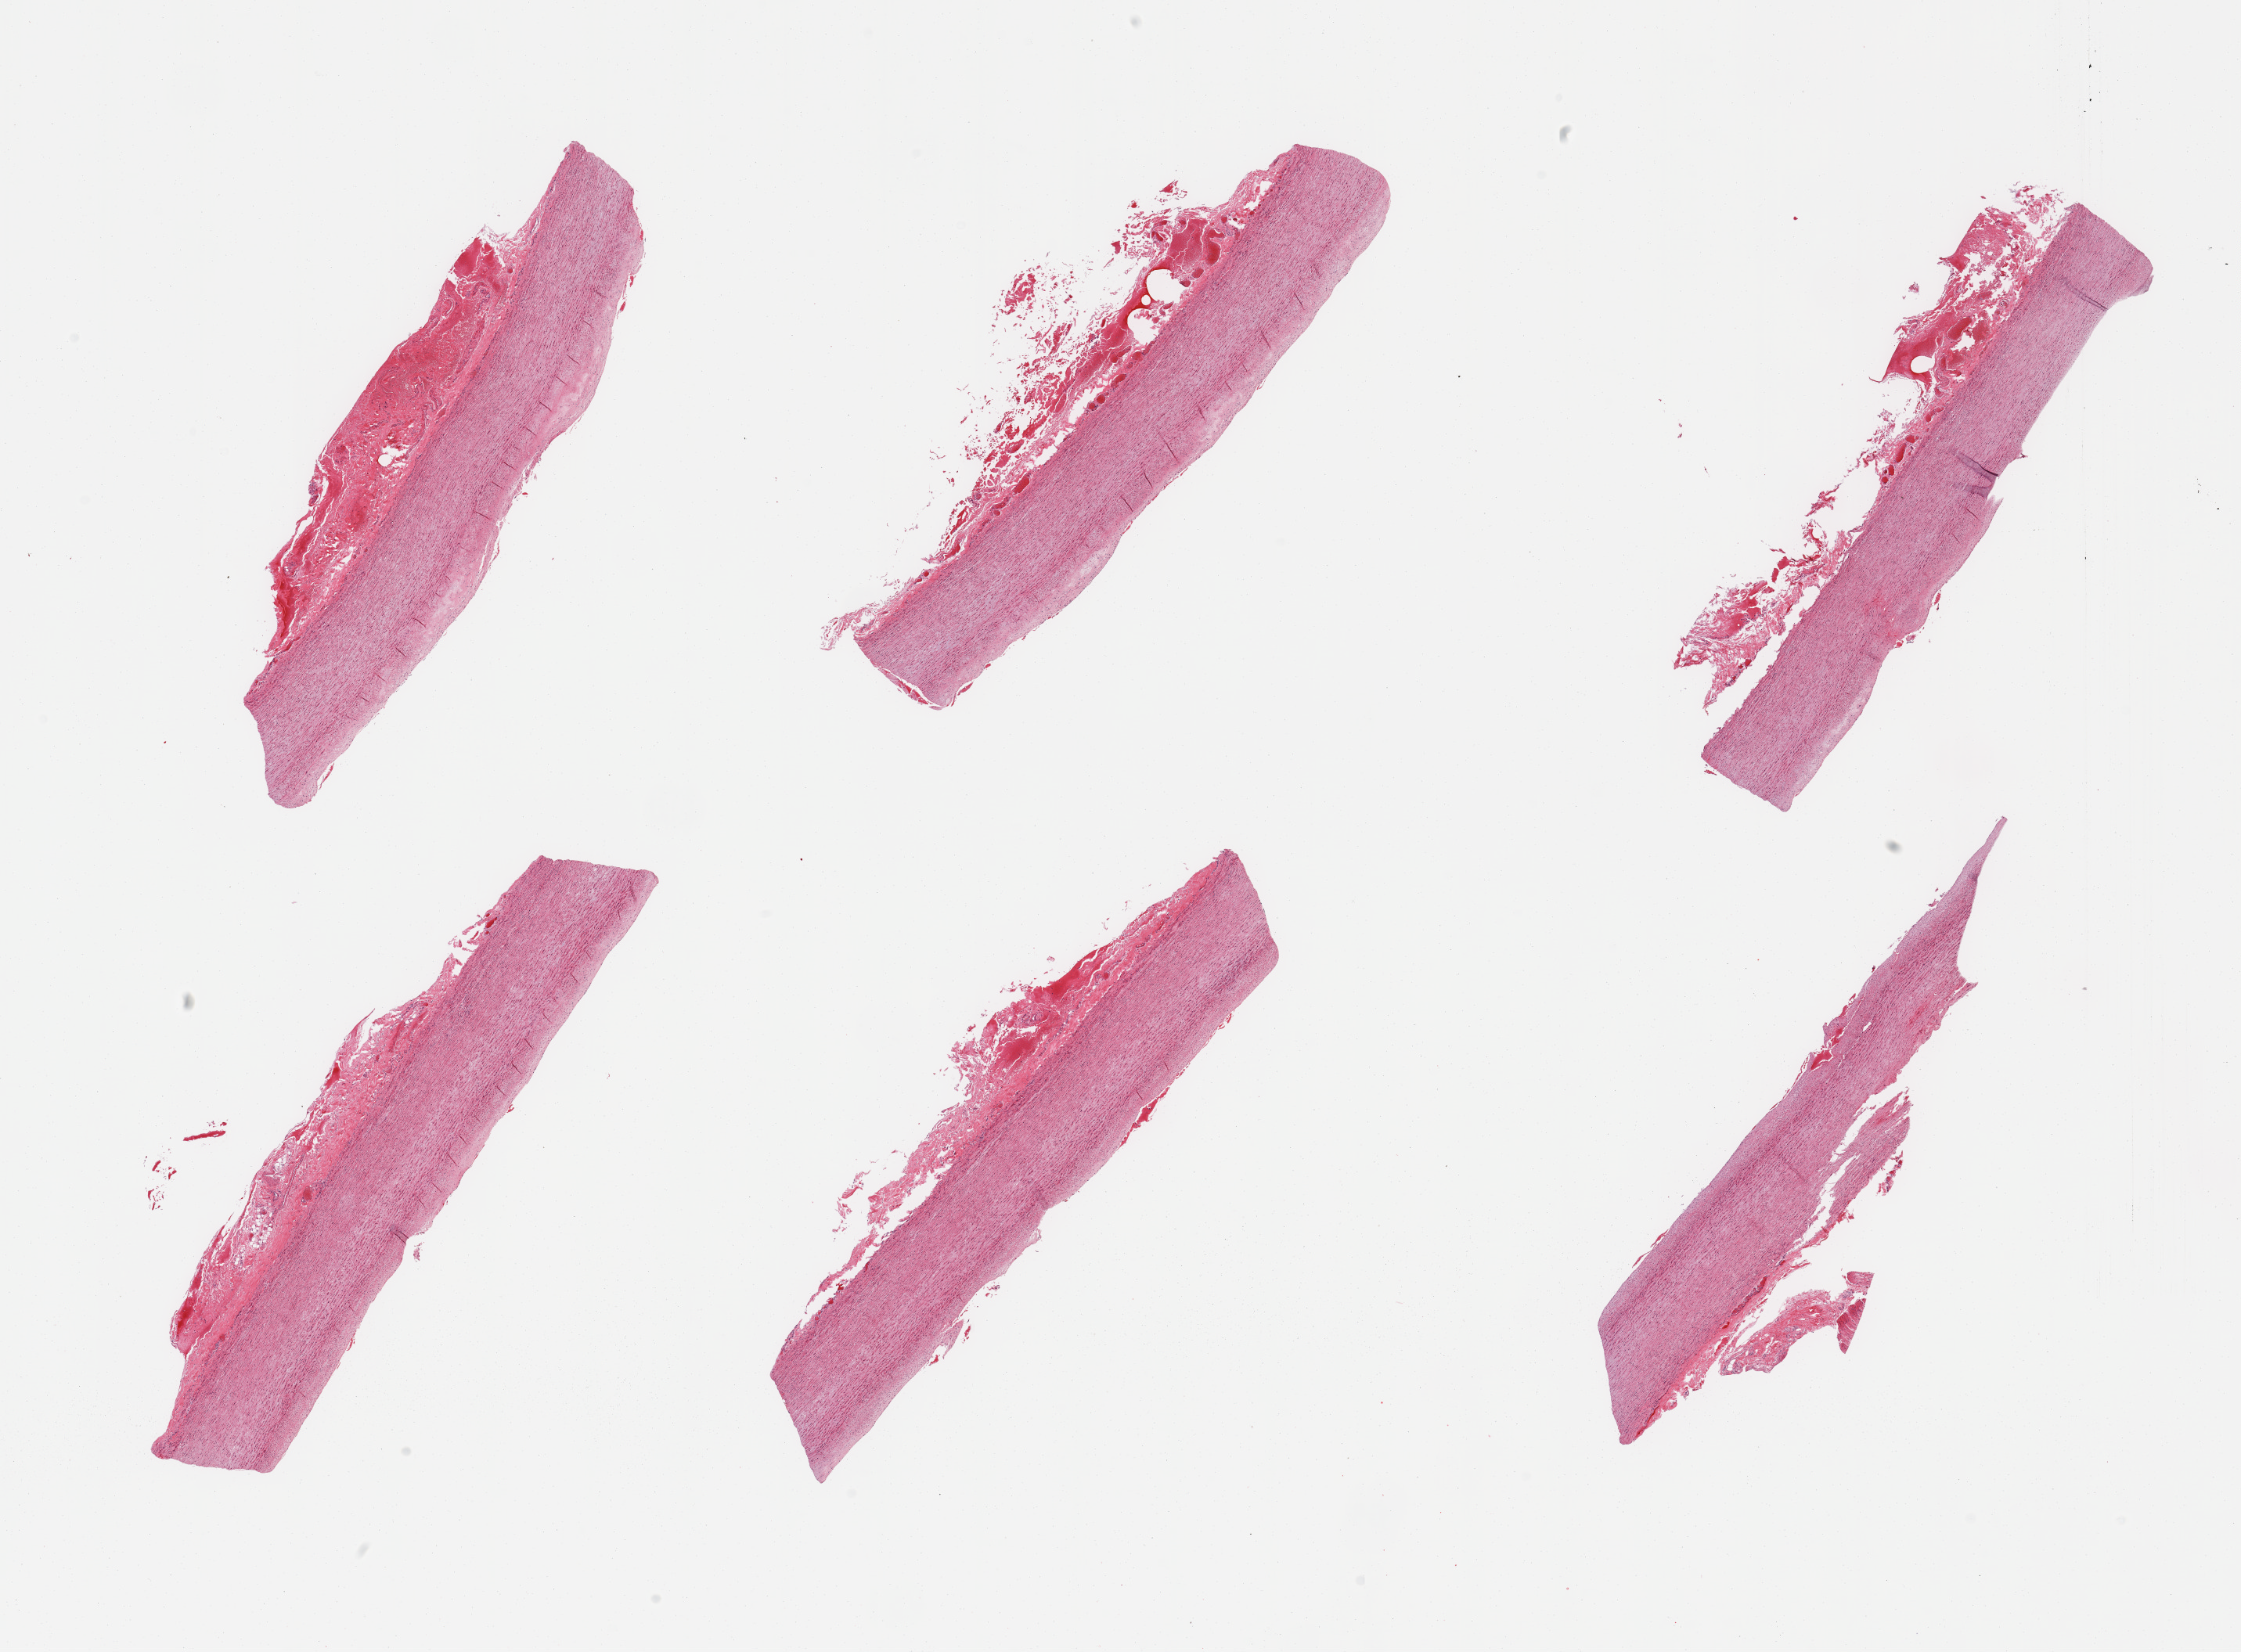
Digitized H&E-stained section, brightfield, shown as a low-resolution overview of the whole scanned area (about 22.6 x 16.7 mm). PAXgene-fixed, paraffin-embedded tissue. Target tissue: aorta. Tissue donor sample. Donor: female.
• pathologist's review note for this sample: 6 pieces; slight flat plaques; fibrous adventitia up to 0.8 mm thick with focal hemorrhage